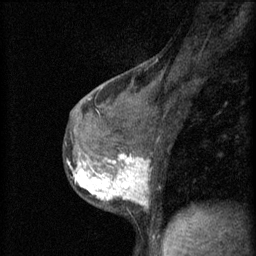
Breast MRI (dynamic contrast-enhanced), one sagittal slice; slice 33 of 60 in the series (ordered by position); 3 images stored at this slice position (order not interpretable as contrast timing); 1.5 T; TE 4.2 ms, TR 11 ms; 2 mm slice thickness; 256 × 256 image matrix. Female patient, age 37 years.
Structures marked on this image (semi-automatic segmentation, software-assisted and operator-edited):
- analysis volume of interest (the breast-tissue region the enhancement analysis was run in; not a lesion): bounding box <65,138,154,211> (left, top, right, bottom; pixels)
- tumour enhancement mask (voxels above the 70 % enhancement threshold inside the analysis volume of interest): <68,154,149,205>